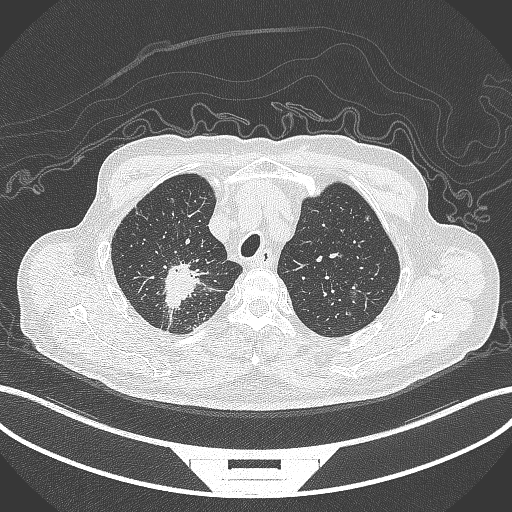
Chest CT, one axial slice. Slice 311 of 407 in the series (ordered by position). Reconstruction kernel B70f. 120 kVp. Lung window (W 1500 / L -600 HU). 1 mm slice thickness. 512 × 512 image matrix, field of view 400 × 400 mm. Male patient, age 69 years. From the clinical record (not read from this slice): clinical TNM (as recorded): T1c N1 M1.
Annotated regions visible in this slice (bounding box drawn by a radiologist):
- lung tumour (recorded histology: adenocarcinoma): bounding box [x1, y1, x2, y2] px = [158, 257, 206, 318]